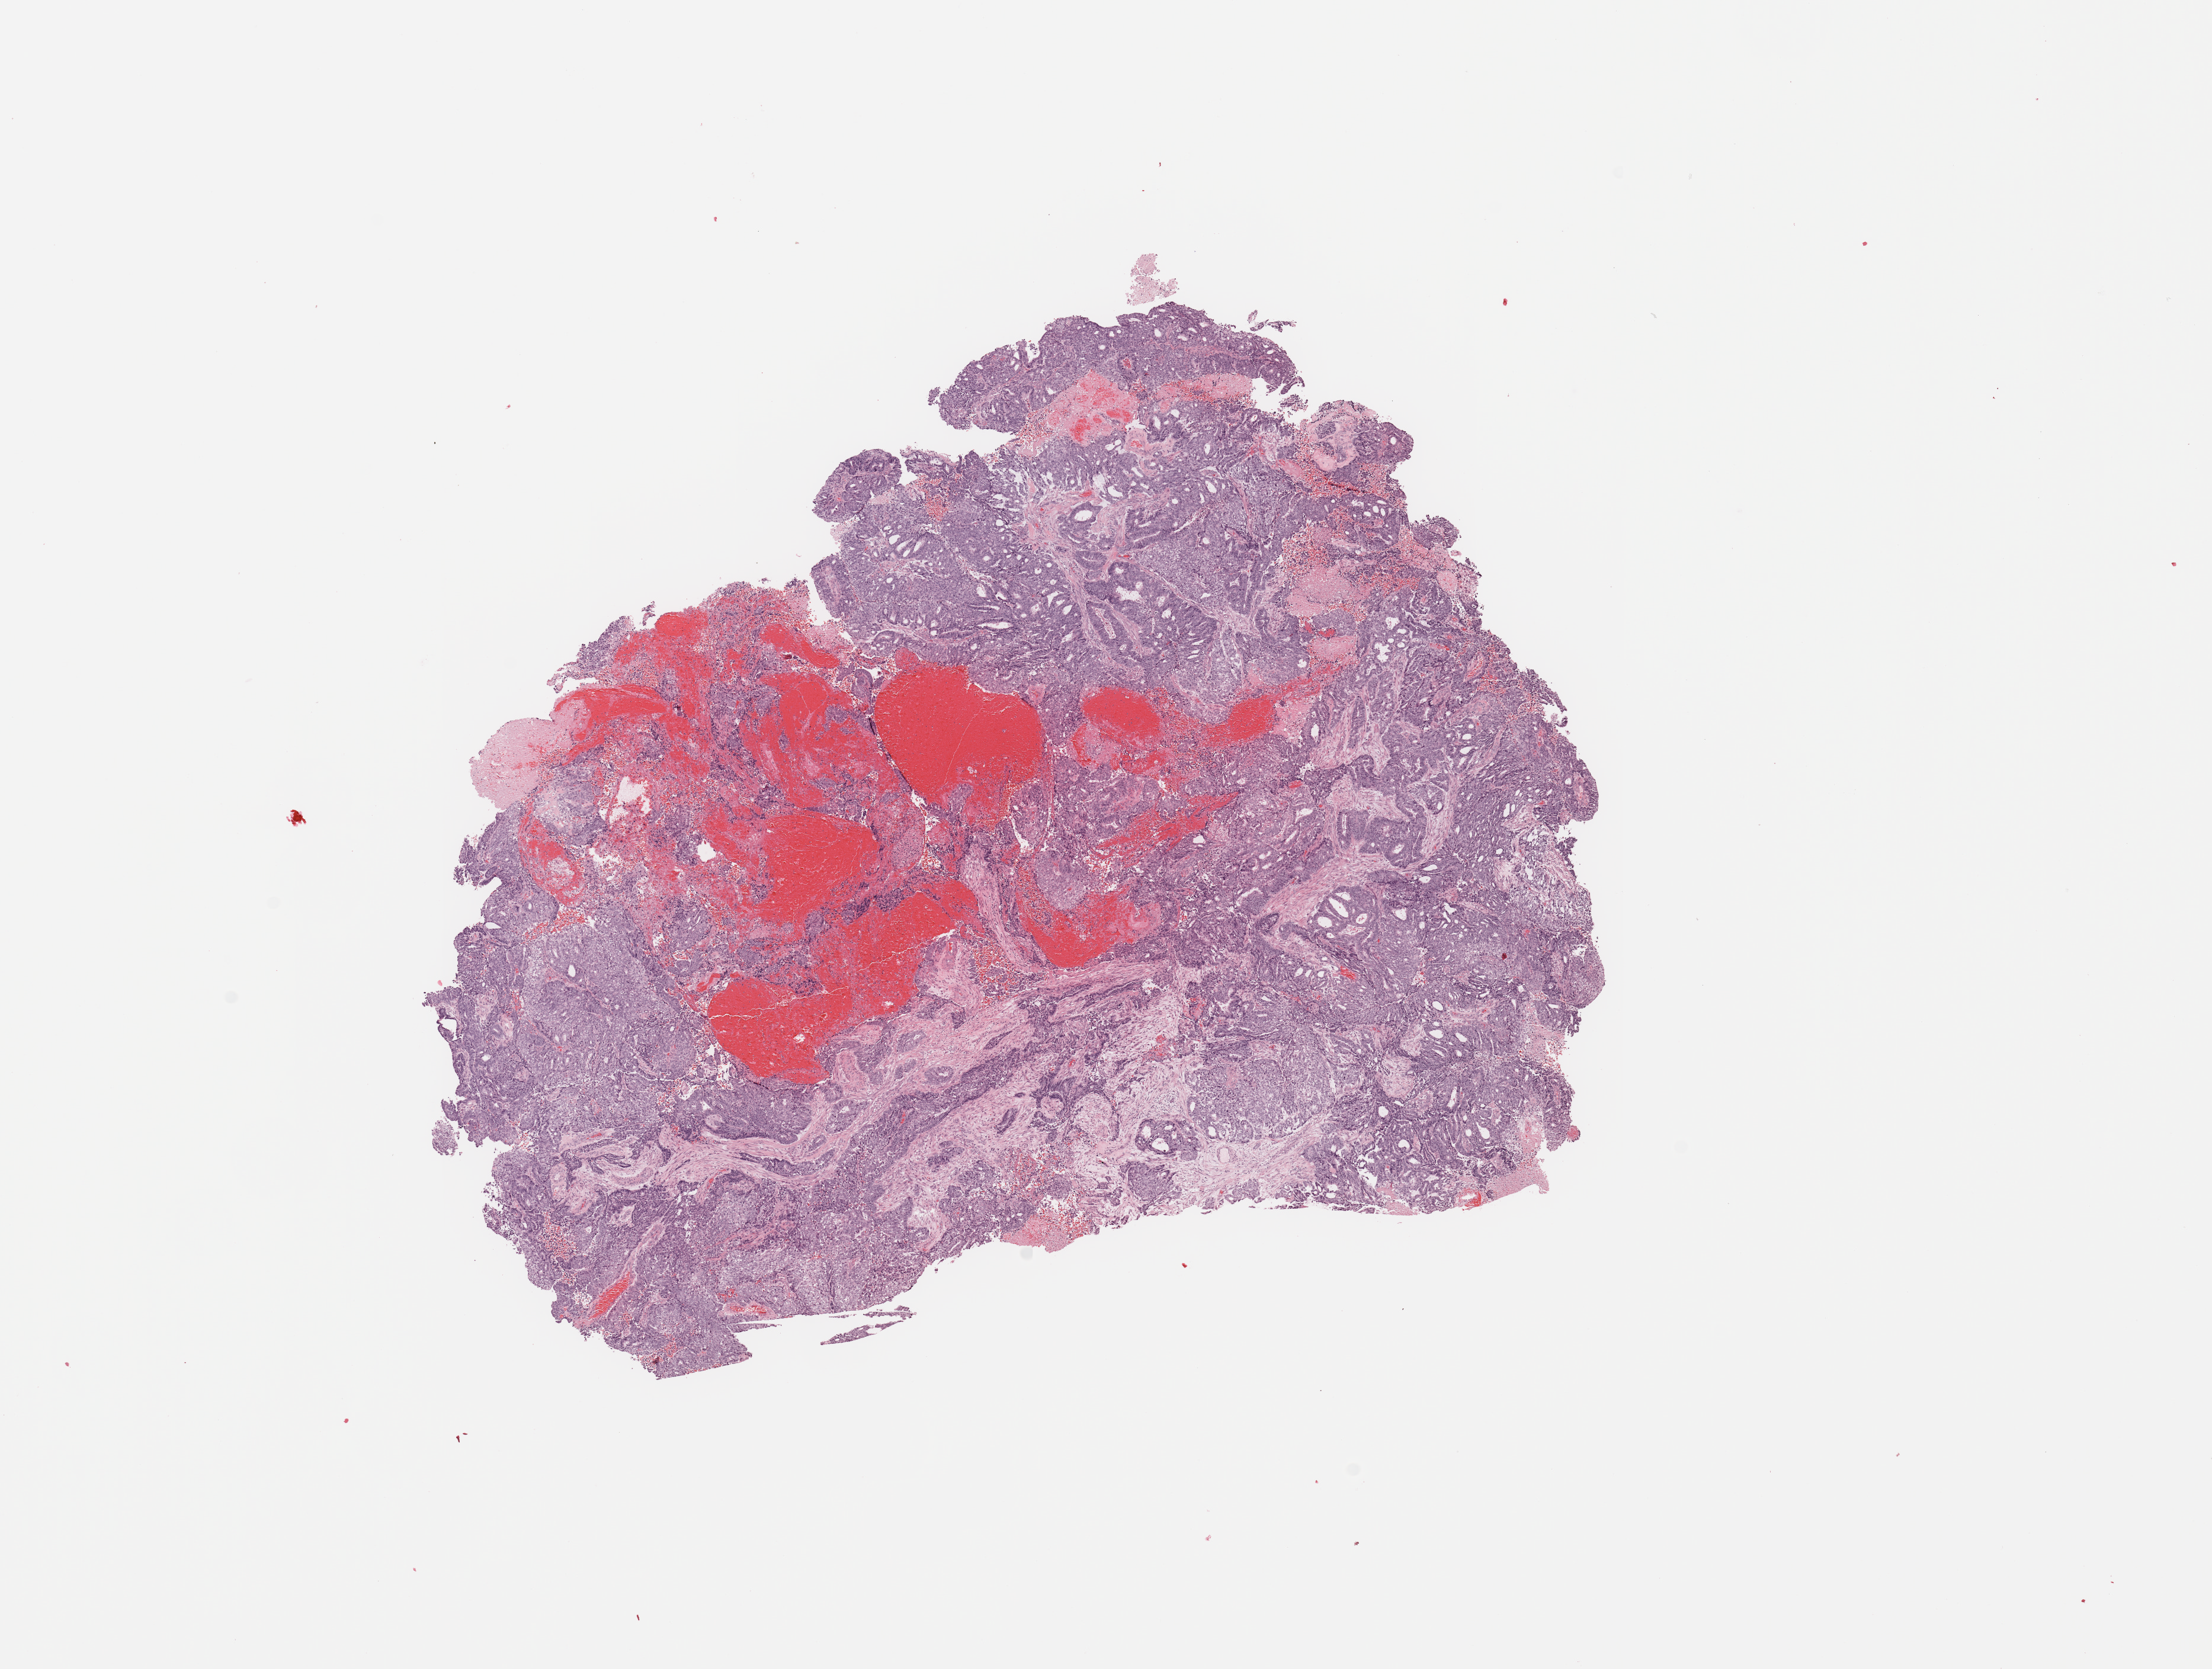
H&E-stained whole-slide image, whole scanned area (about 14.8 x 11.1 mm, slide scanned at 20x) shown as a low-resolution overview. Tumour tissue sample, sampled site: uterus. Female, 78 y/o. Histologic grade: G2 (moderately differentiated). Composition of this section per pathologist review: tumour nuclei 80%, necrosis 2%.
• AJCC pathologic stage: I
• diagnosis: Endometrioid adenocarcinoma, NOS
• primary tumour site (as recorded): posterior endometrium